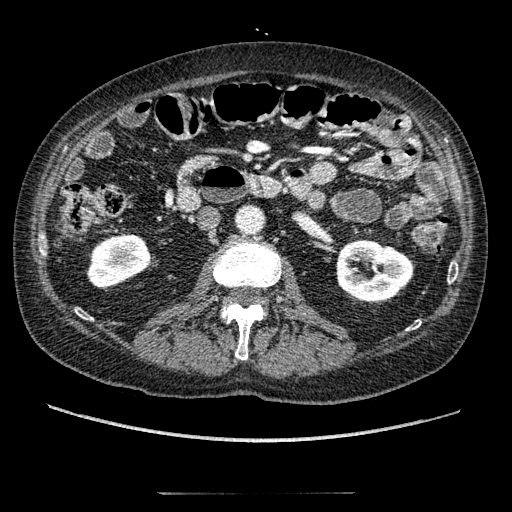
Contrast-enhanced abdominal CT, one axial slice. Position 76 of 274 along the scan axis. 120 kVp. Intravenous contrast given. Soft-tissue window (W 400 / L 40 HU). 512 × 512 image matrix. Patient: male, 69 years. Case-level facts recorded for this patient, not image findings: diagnosis: adrenocortical carcinoma; tumour side: left adrenal; tumour size at pathology: 6.1 cm.
Outlined on this slice (semi-automatically segmented with operator editing):
- mass: bounding box (x1, y1, x2, y2) in pixels: (310, 192, 325, 207)